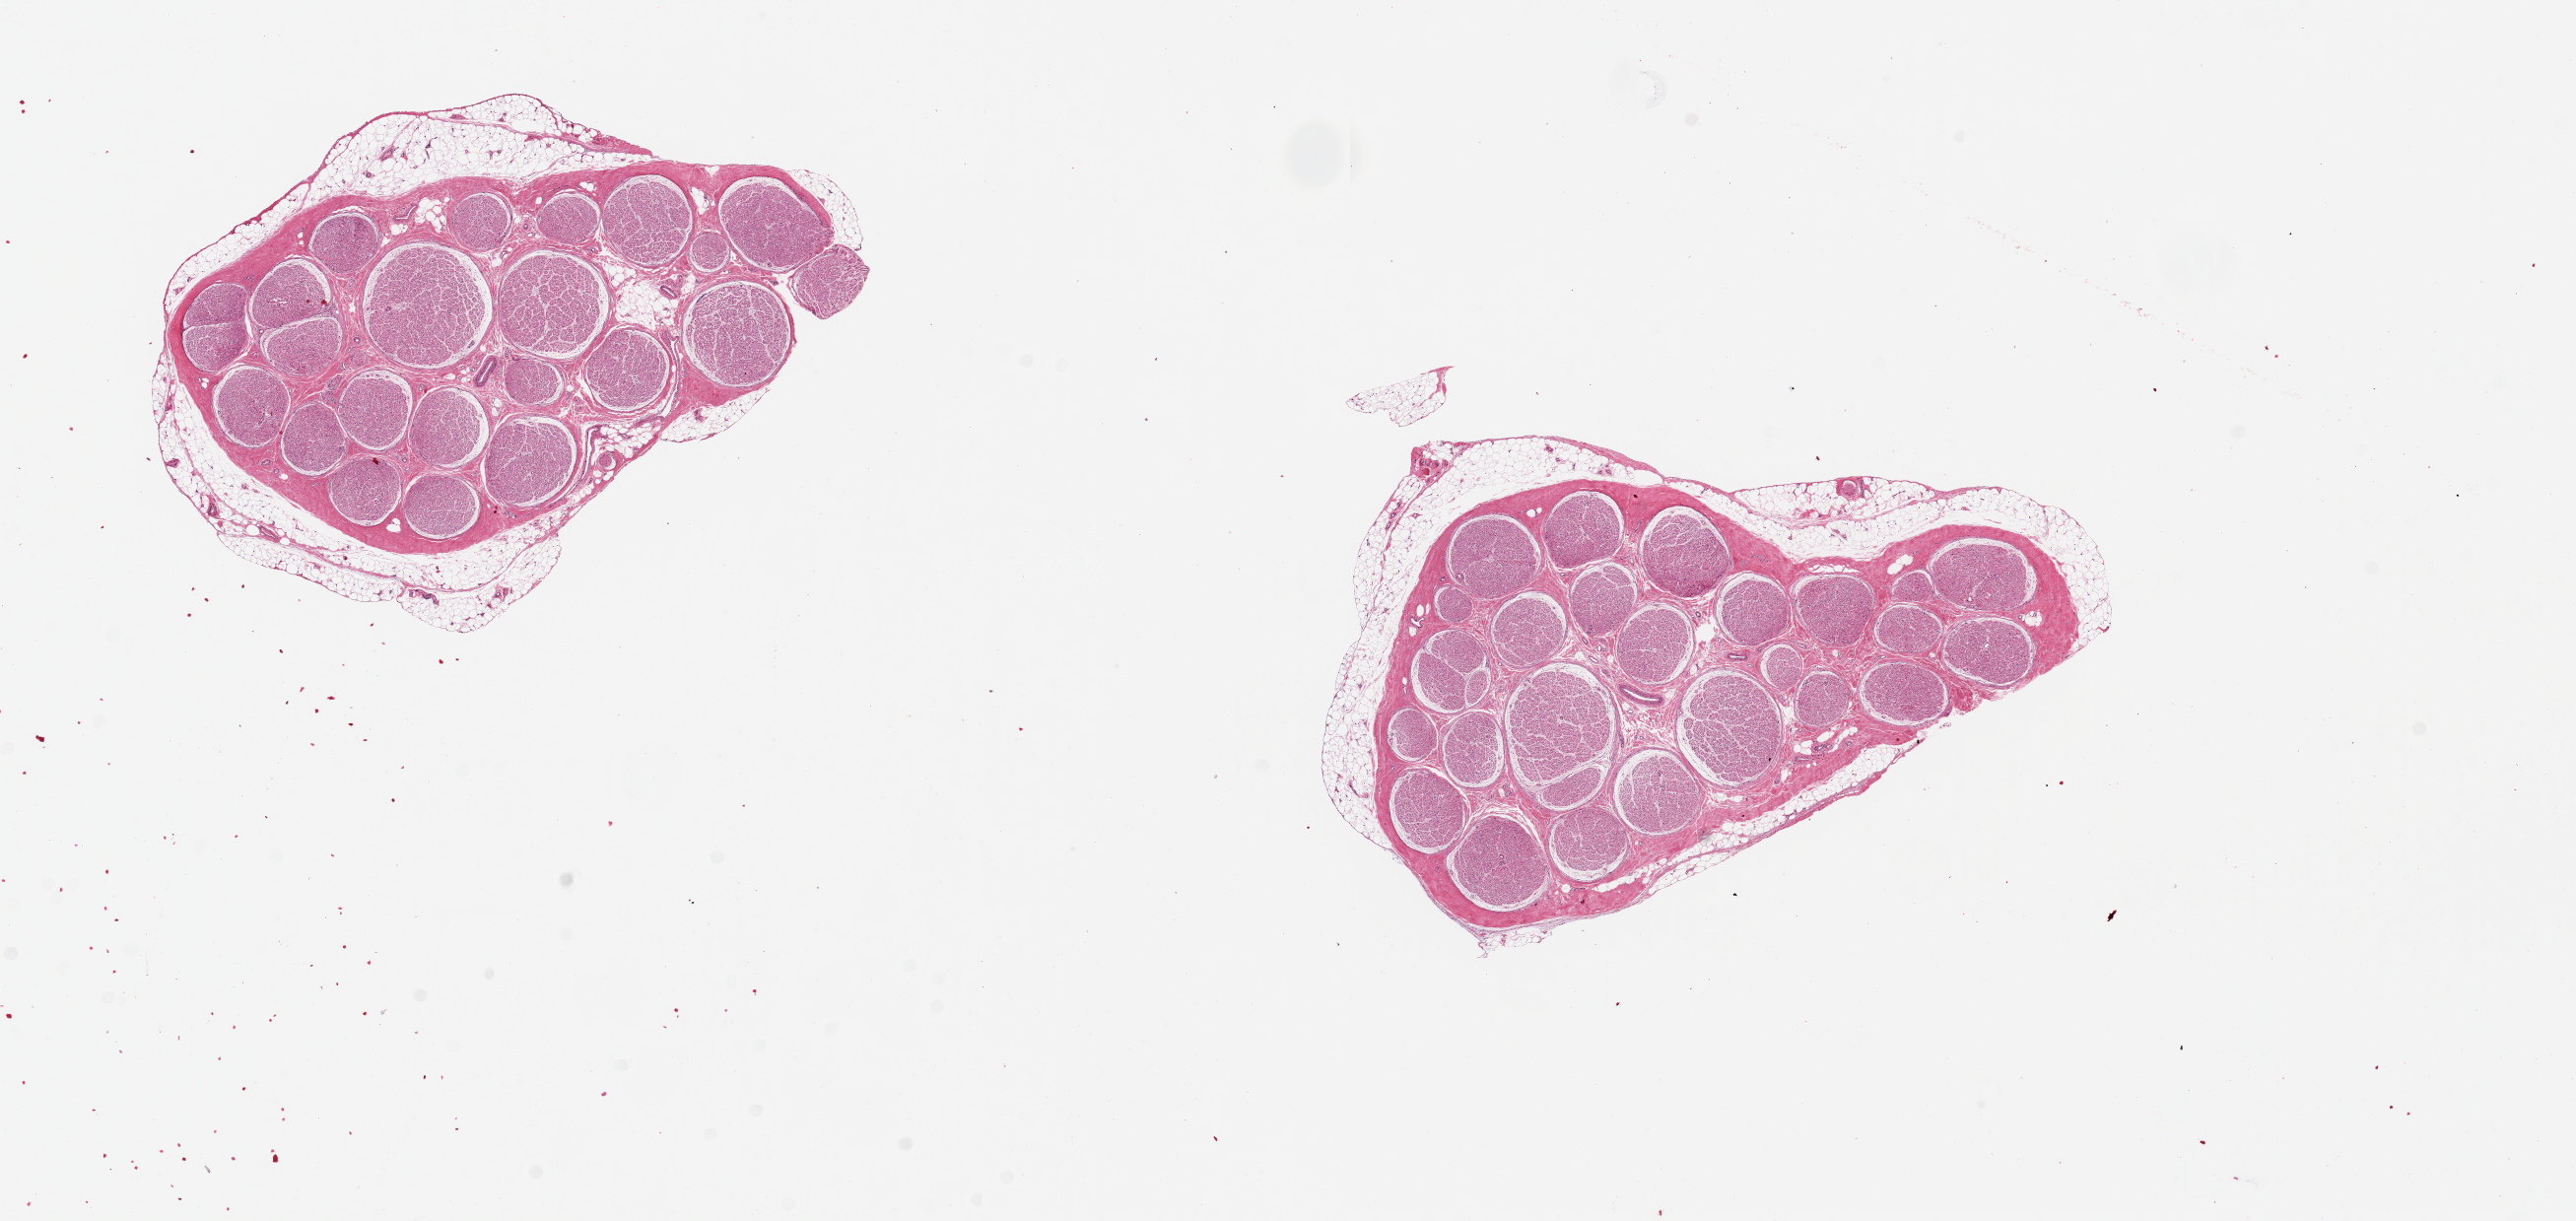
Hematoxylin and eosin (H&E) whole-slide image — low-resolution overview of the scanned area, about 20.7 x 9.8 mm. PAXgene-fixed paraffin-embedded (PFPE) section. Target tissue: tibial nerve. Tissue donor sample.
Review note (as recorded): 2 pieces, 6x4 & 6x5mm; discontinous rim of adherent fat up to ~0.5mm.